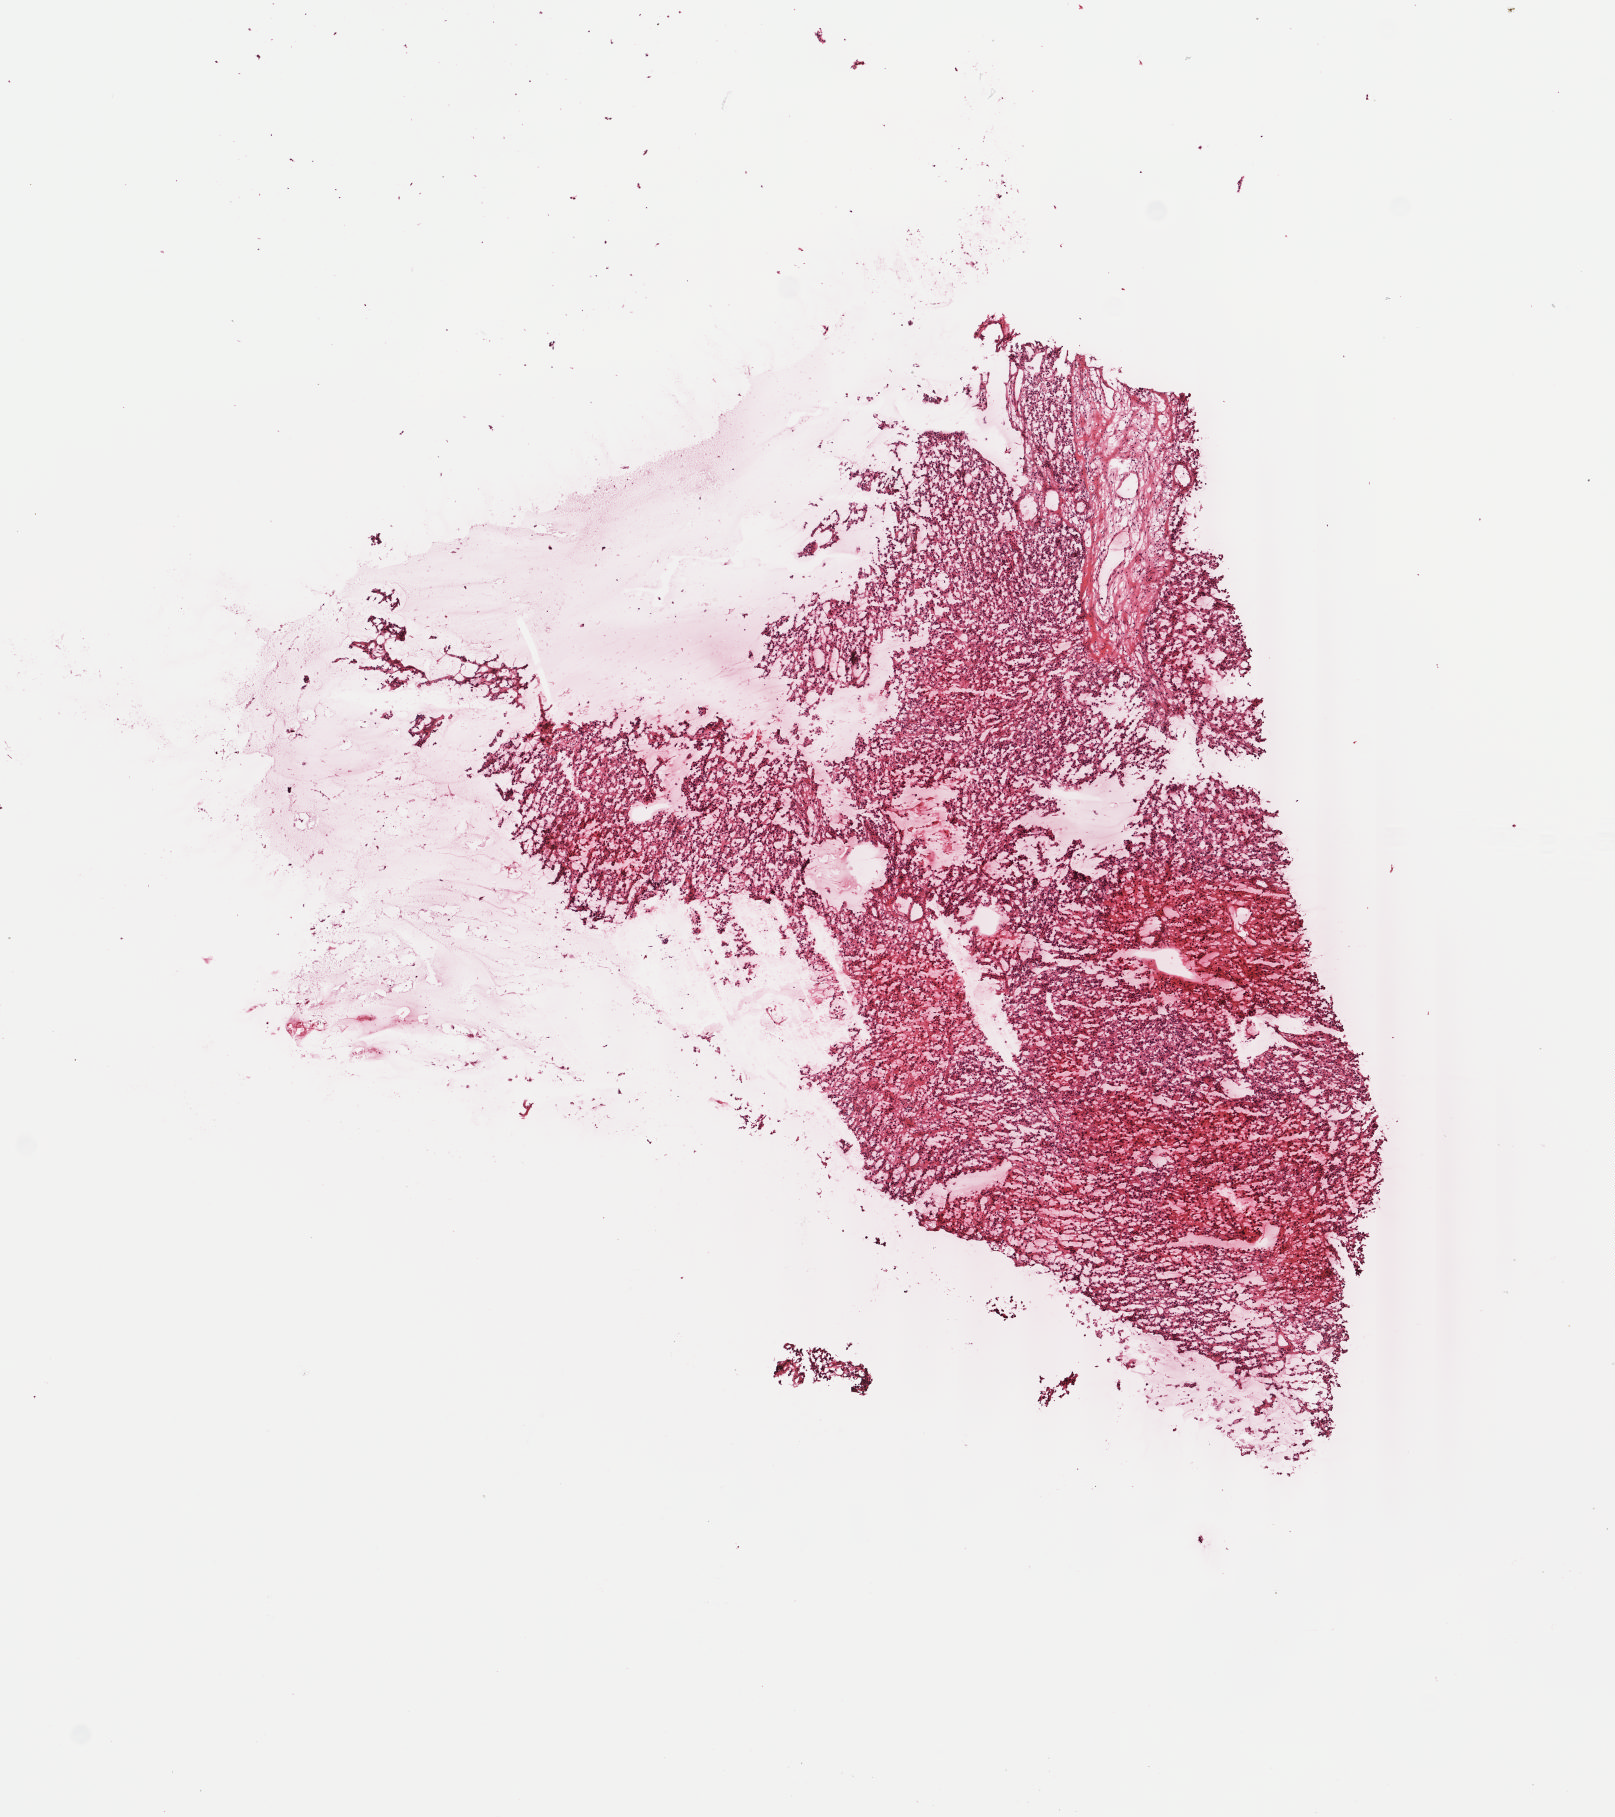
Whole-slide histology image, H&E, low-resolution overview of the scanned area, about 6.4 x 7.2 mm (from a 40x scan), frozen section, sample: primary tumour, adrenal cortex. Female, age 26 years at initial diagnosis. Slide review estimates, as recorded: tumour cells 95%, tumour nuclei 90%, normal cells 0%, stromal cells 5%, necrosis 0%. Inflammatory infiltration, as recorded: lymphocyte infiltration 5%, monocyte infiltration 0%, neutrophil infiltration 0%.
Diagnosis: Adrenal cortical carcinoma (cortex of adrenal gland).